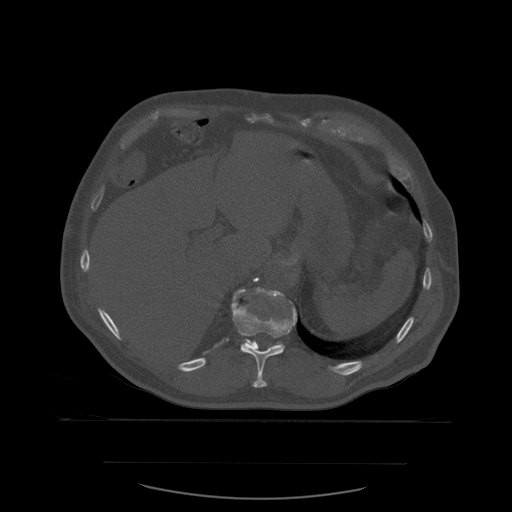
CT including the spine, one axial slice; slice 291 of 590 in the series (ordered by position); bone window (W 1800 / L 400 HU); 1.25 mm slice thickness; 512 × 512 image matrix, field of view 479 × 479 mm. Patient age 71 years. Case-level facts recorded for this patient, not image findings: primary cancer: lung; vertebrae with lytic lesions (as recorded): T1, T2, L5, S1.
Structures marked on this image (semi-automatic segmentation, software-assisted and operator-edited):
- T11 vertebra: bounding box [x1, y1, x2, y2] px = [232, 289, 298, 388]
- T12 vertebra: [231, 288, 292, 346]